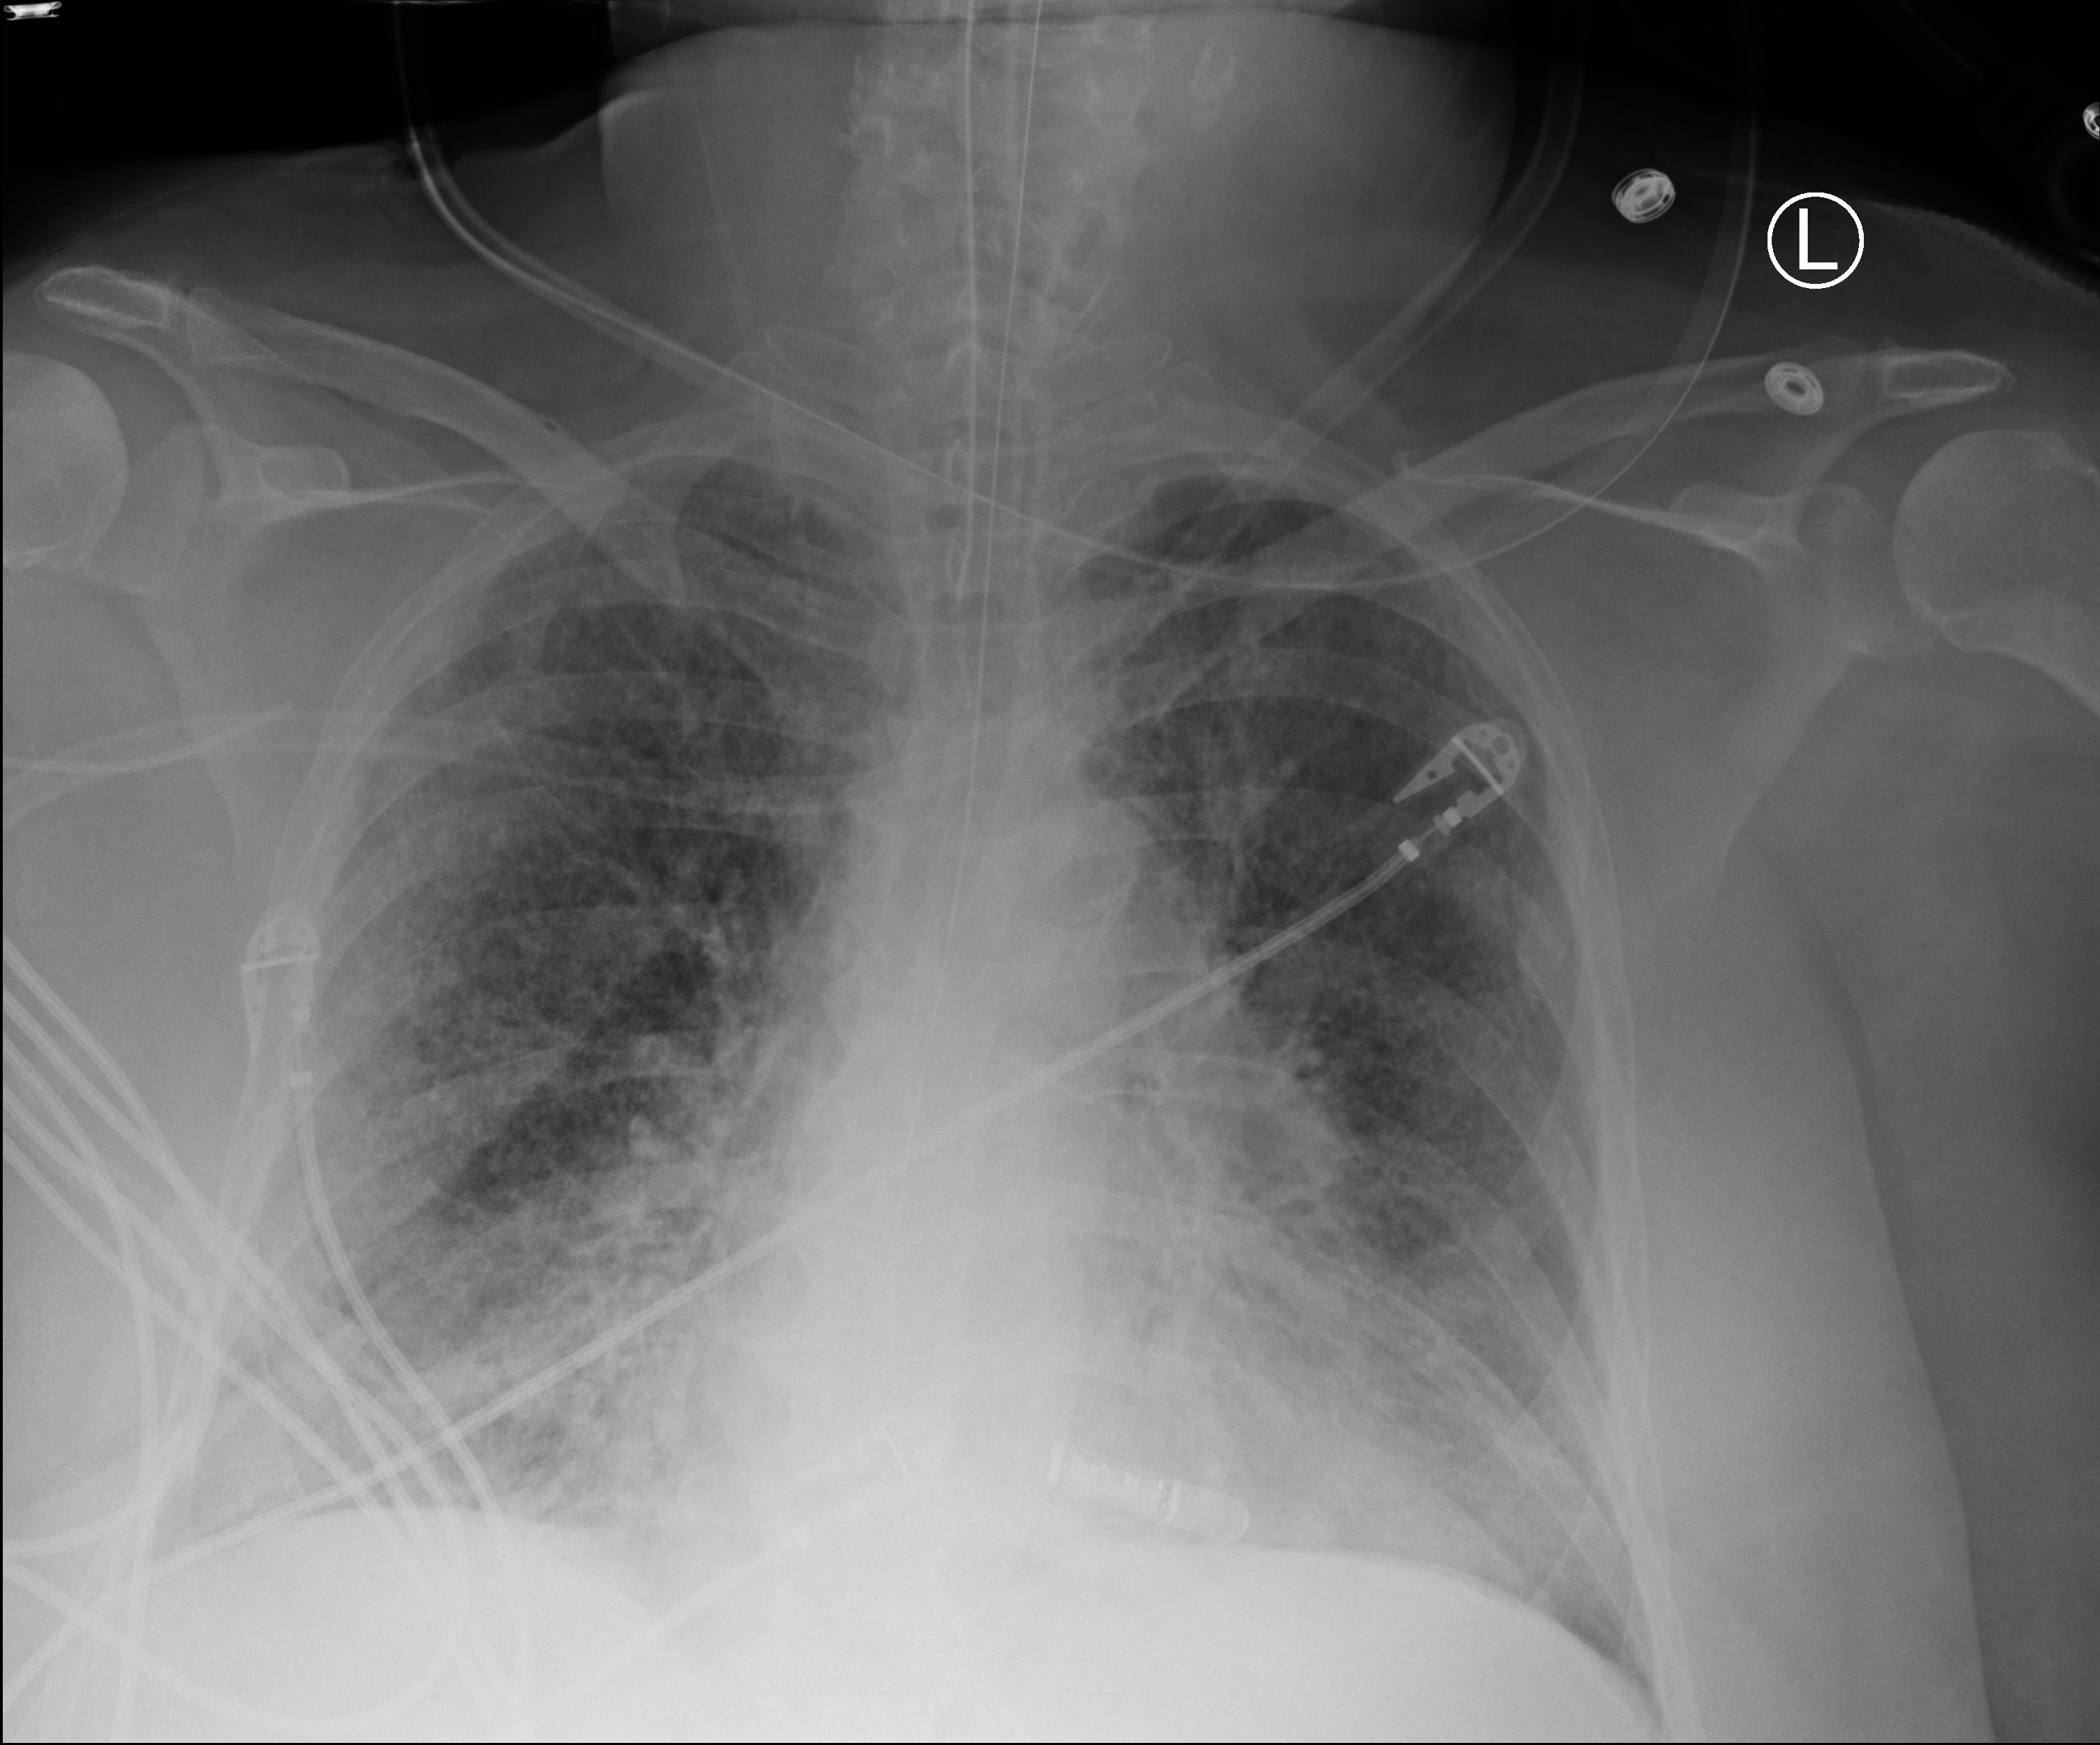
Portable chest radiograph; anteroposterior (AP) projection. Female patient hospitalised with COVID-19, age 60–74 years.
From the hospital-stay record, not from the radiograph (when in the stay this image was taken is not recorded):
- length of hospital stay: 28 days
- mechanically ventilated during this hospital stay: yes
- admitted to intensive care during this hospital stay: yes